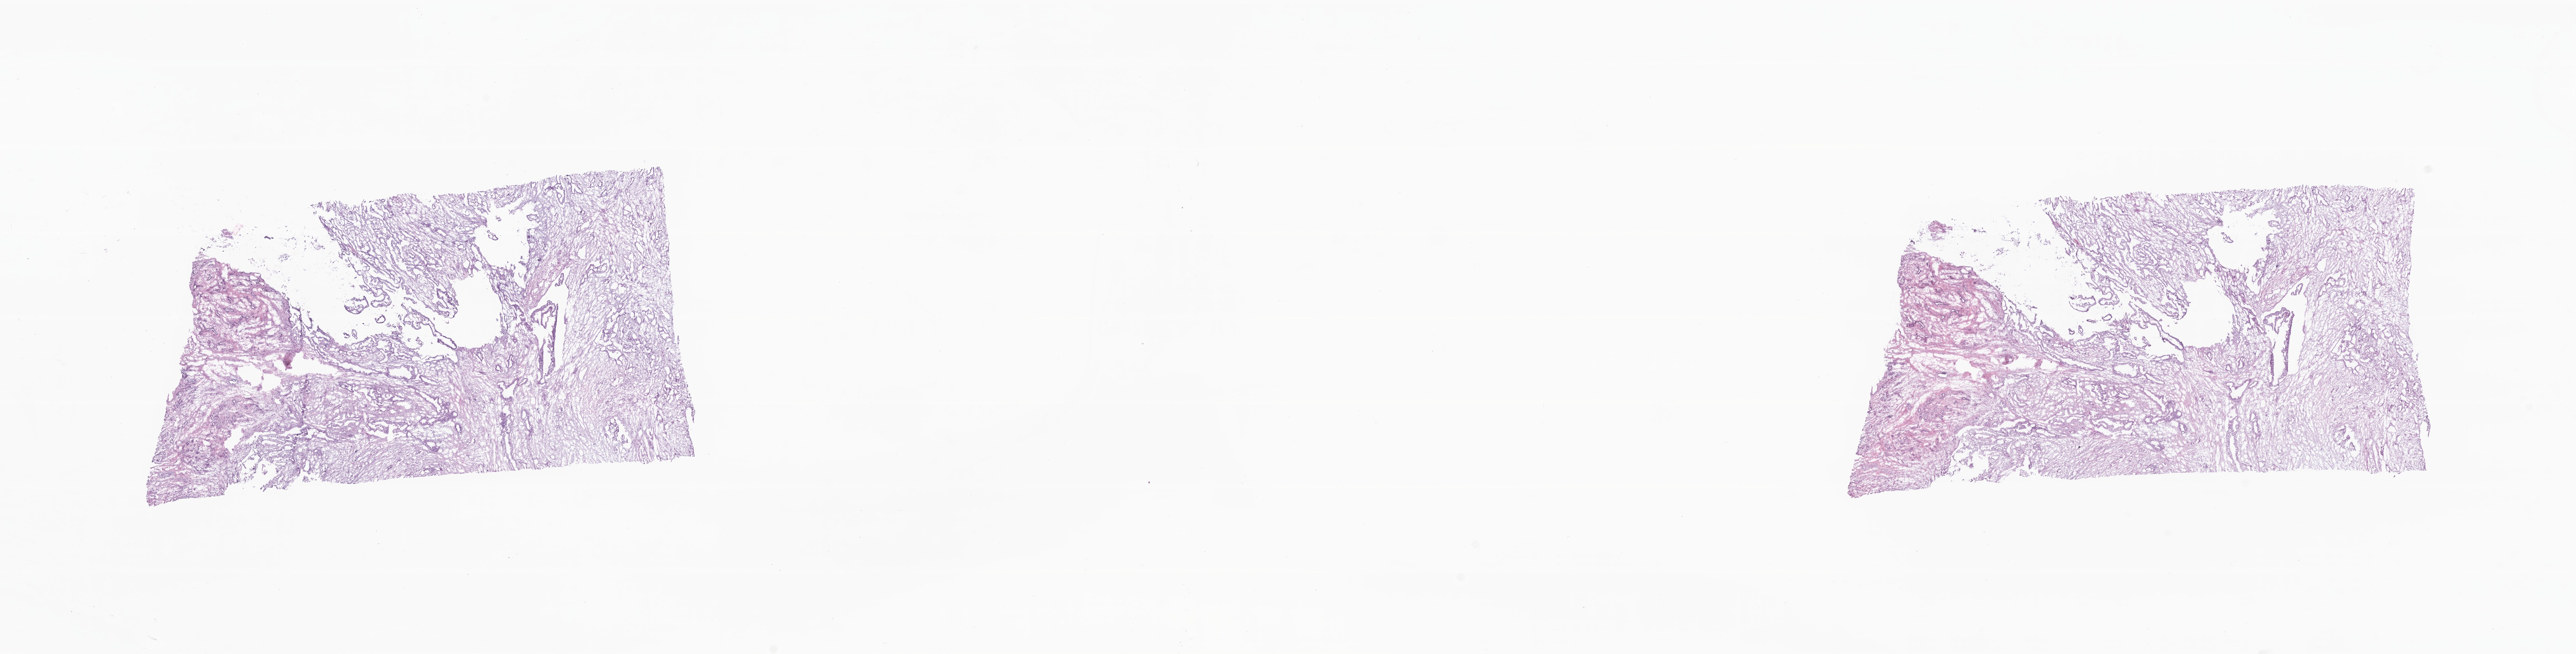
Whole-slide image, hematoxylin and eosin (H&E) stain, a low-resolution overview of the entire scanned area, about 32.5 x 8.2 mm, frozen section (tissue freezing medium), primary tumor, anatomic site: tail of pancreas. Female patient; age at initial diagnosis 62 years. Pathologist review of this section (percent, as recorded): tumor cells 40%, tumor nuclei 50%, stromal cells 60%, necrosis 0%, normal cells 0%. Inflammatory infiltration, as recorded: lymphocyte infiltration 0%, monocyte infiltration 0%, neutrophil infiltration 0%.
• histologic diagnosis: Infiltrating duct carcinoma, NOS